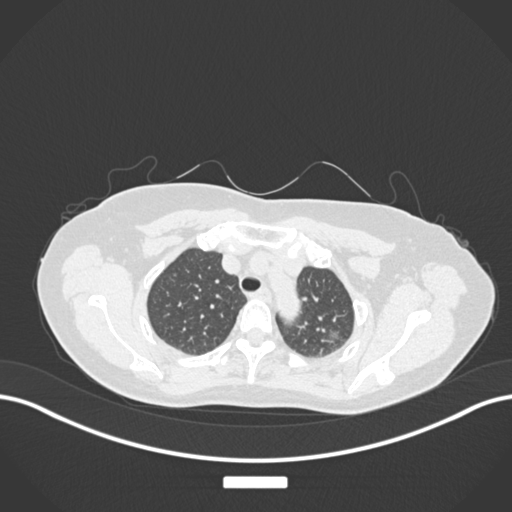
Chest CT, one axial slice. Position 139 of 181 along the scan axis. Lung window (W 1500 / L -600 HU). 1 mm slice thickness. 512 × 512 image matrix, field of view 400 × 400 mm. Female patient, age 58 years. From the clinical record (not read from this slice): clinical TNM (as recorded): T1c N0 M0.
Structures marked on this image (rectangle marked by the reading radiologist):
- lung tumour (recorded histology: adenocarcinoma): bounding box [x1, y1, x2, y2] px = [320, 327, 344, 349]